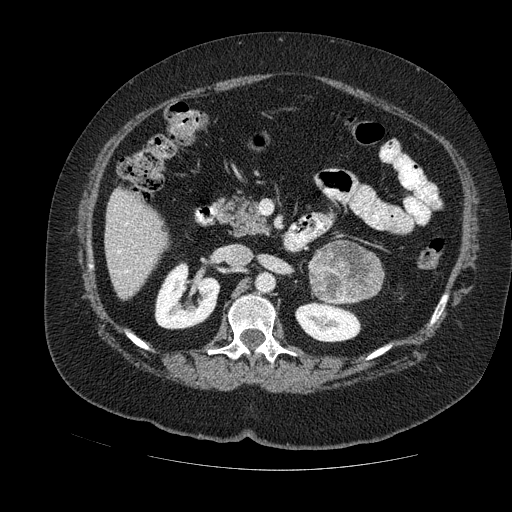
Contrast-enhanced abdominal CT, one axial slice; slice 61 of 121 in the series (ordered by position); soft-tissue window (W 400 / L 40 HU); 2.5 mm slice thickness; 512 × 512 image matrix. Female patient. From the clinical record (not read from this slice): diagnosis: adrenocortical carcinoma; tumour side: left adrenal; tumour size at pathology: 8 cm; Ki-67 index: 7 %; stage (as recorded): 2.
Annotated regions visible in this slice (semi-automatically segmented with operator editing):
- mass: box from (x=311, y=243) to (x=382, y=304) px